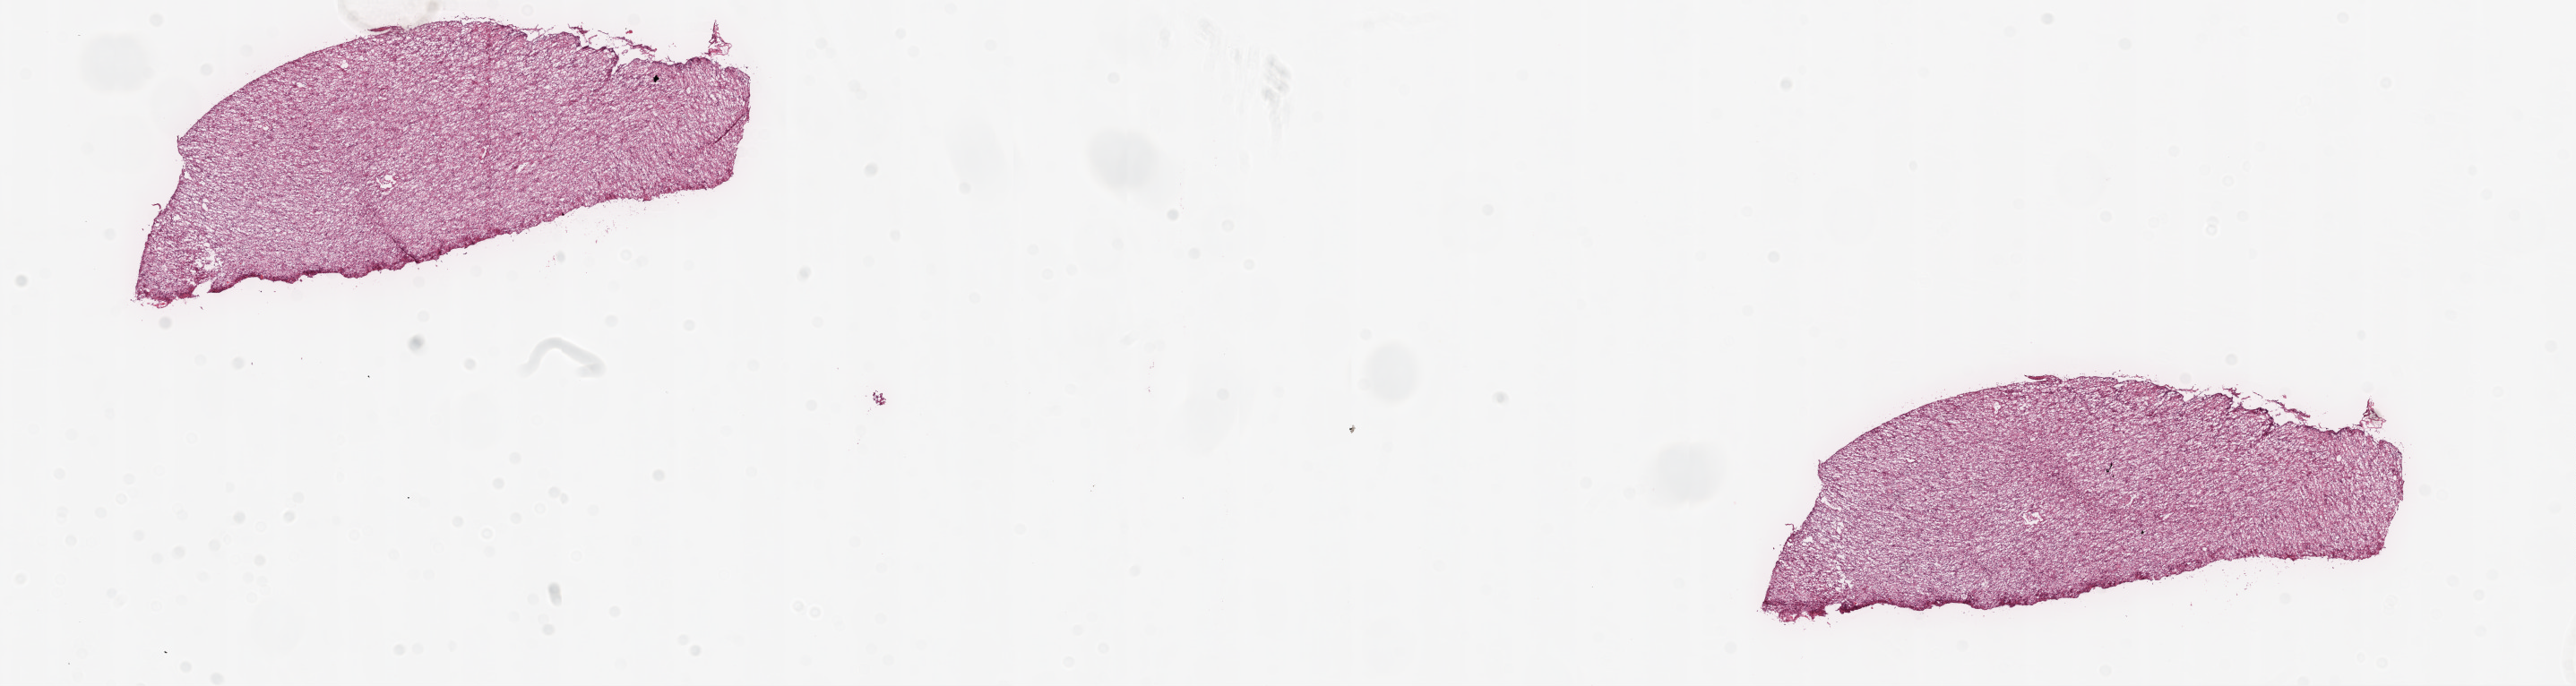
Digitized Hematoxylin and eosin (H&E) stained tissue section (whole slide) — shown as a low-resolution overview of the whole scanned area (about 23.1 x 6.1 mm, from a 20x scan), frozen section from the top of the tissue portion, sample: primary tumour, brain. Male patient; age at initial diagnosis 70 years. Pathologist review of this section (percent, as recorded): tumour cells 100%, tumour nuclei 80%, normal cells 0%, stromal cells 0%, necrosis 0%.
Histologic diagnosis: Glioblastoma.